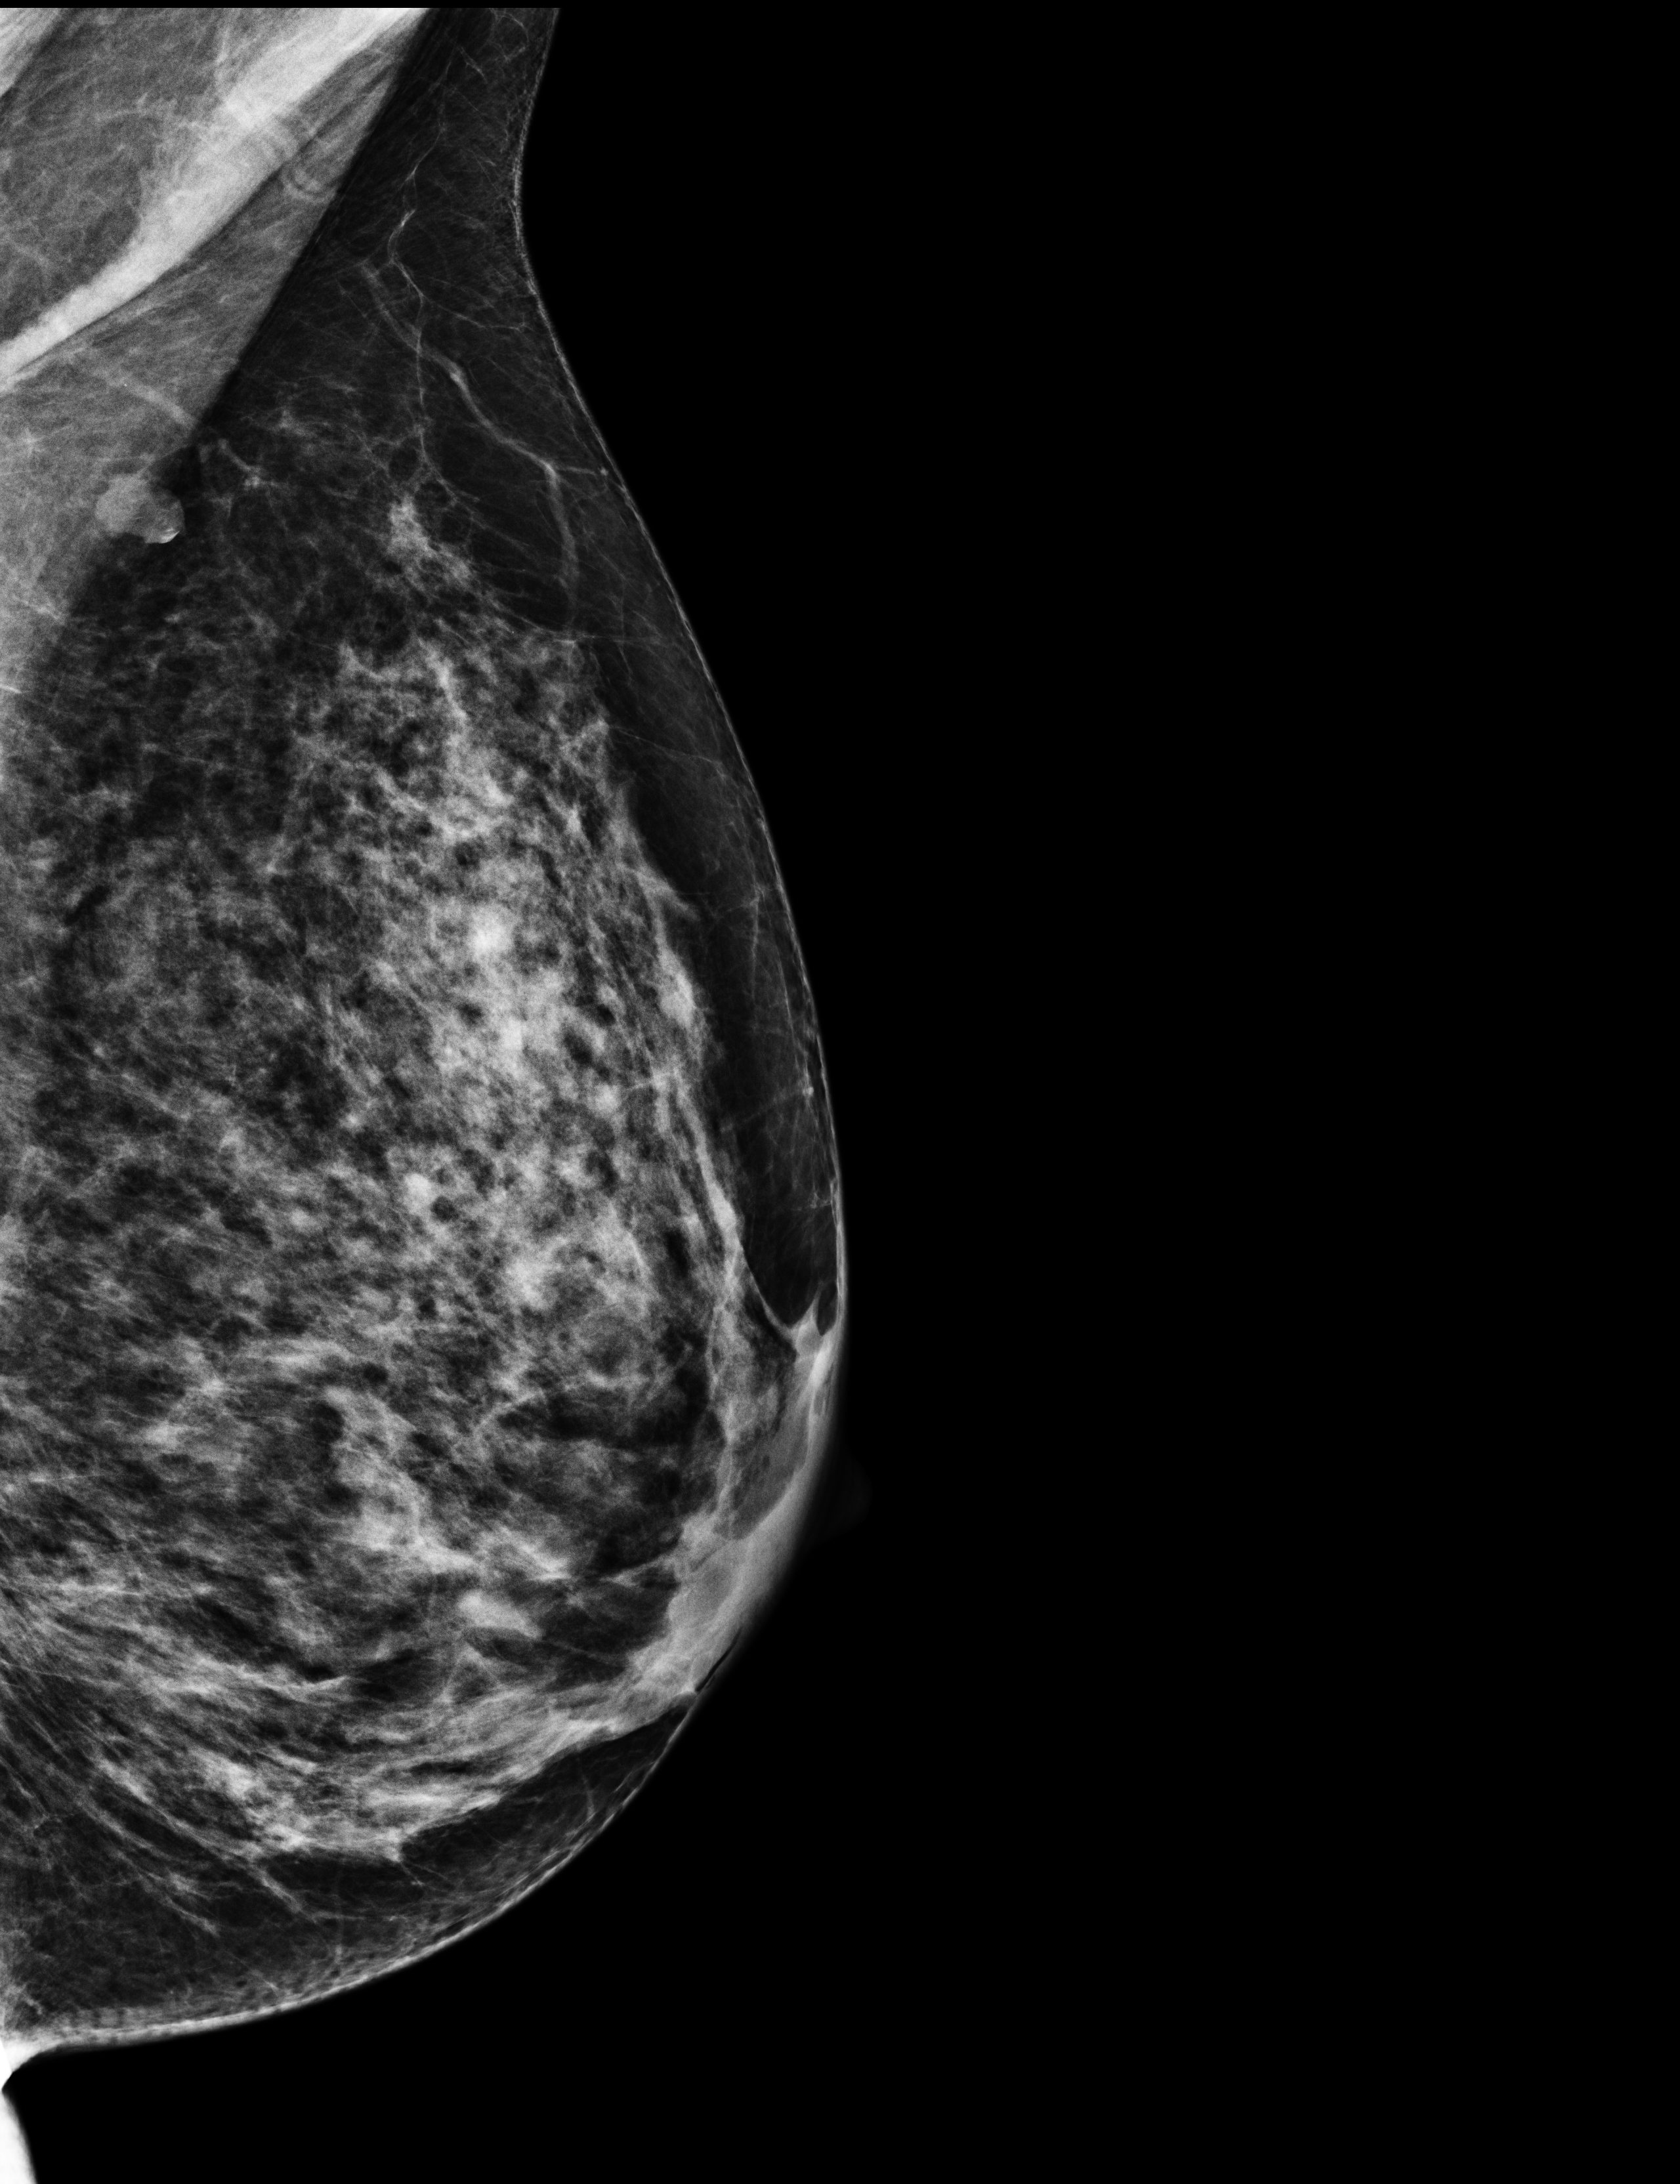
Annual screening mammography examination.
Image type: full-field digital mammogram. Breast: left. Projection: medio-lateral oblique projection.